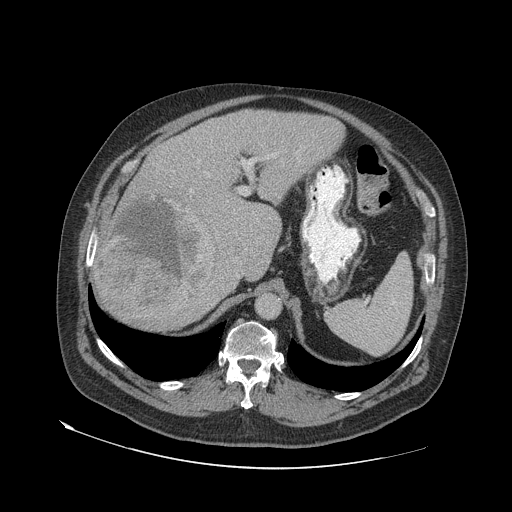
Contrast-enhanced abdominal CT (liver protocol), one axial slice. Reconstruction kernel STANDARD. Soft-tissue window (W 400 / L 40 HU). 2.5 mm slice thickness. 512 × 512 image matrix, field of view 480 × 480 mm. Case-level facts recorded for this patient, not image findings: diagnosis: hepatocellular carcinoma (patient treated with transarterial chemoembolisation; whether this scan precedes or follows treatment is not stated here); TNM stage (as recorded): Stage-IVA; Child-Pugh class: A; tumour differentiation: well differentiated.
Structures marked on this image (semi-automatic segmentation, software-assisted and operator-edited):
- liver parenchyma outside the tumour (the mass and vessels are separate outlines, so this box may not span the whole liver): bounding box <94,110,344,328> (left, top, right, bottom; pixels)
- mass: <99,195,216,321>
- liver vessels: <190,154,274,192>